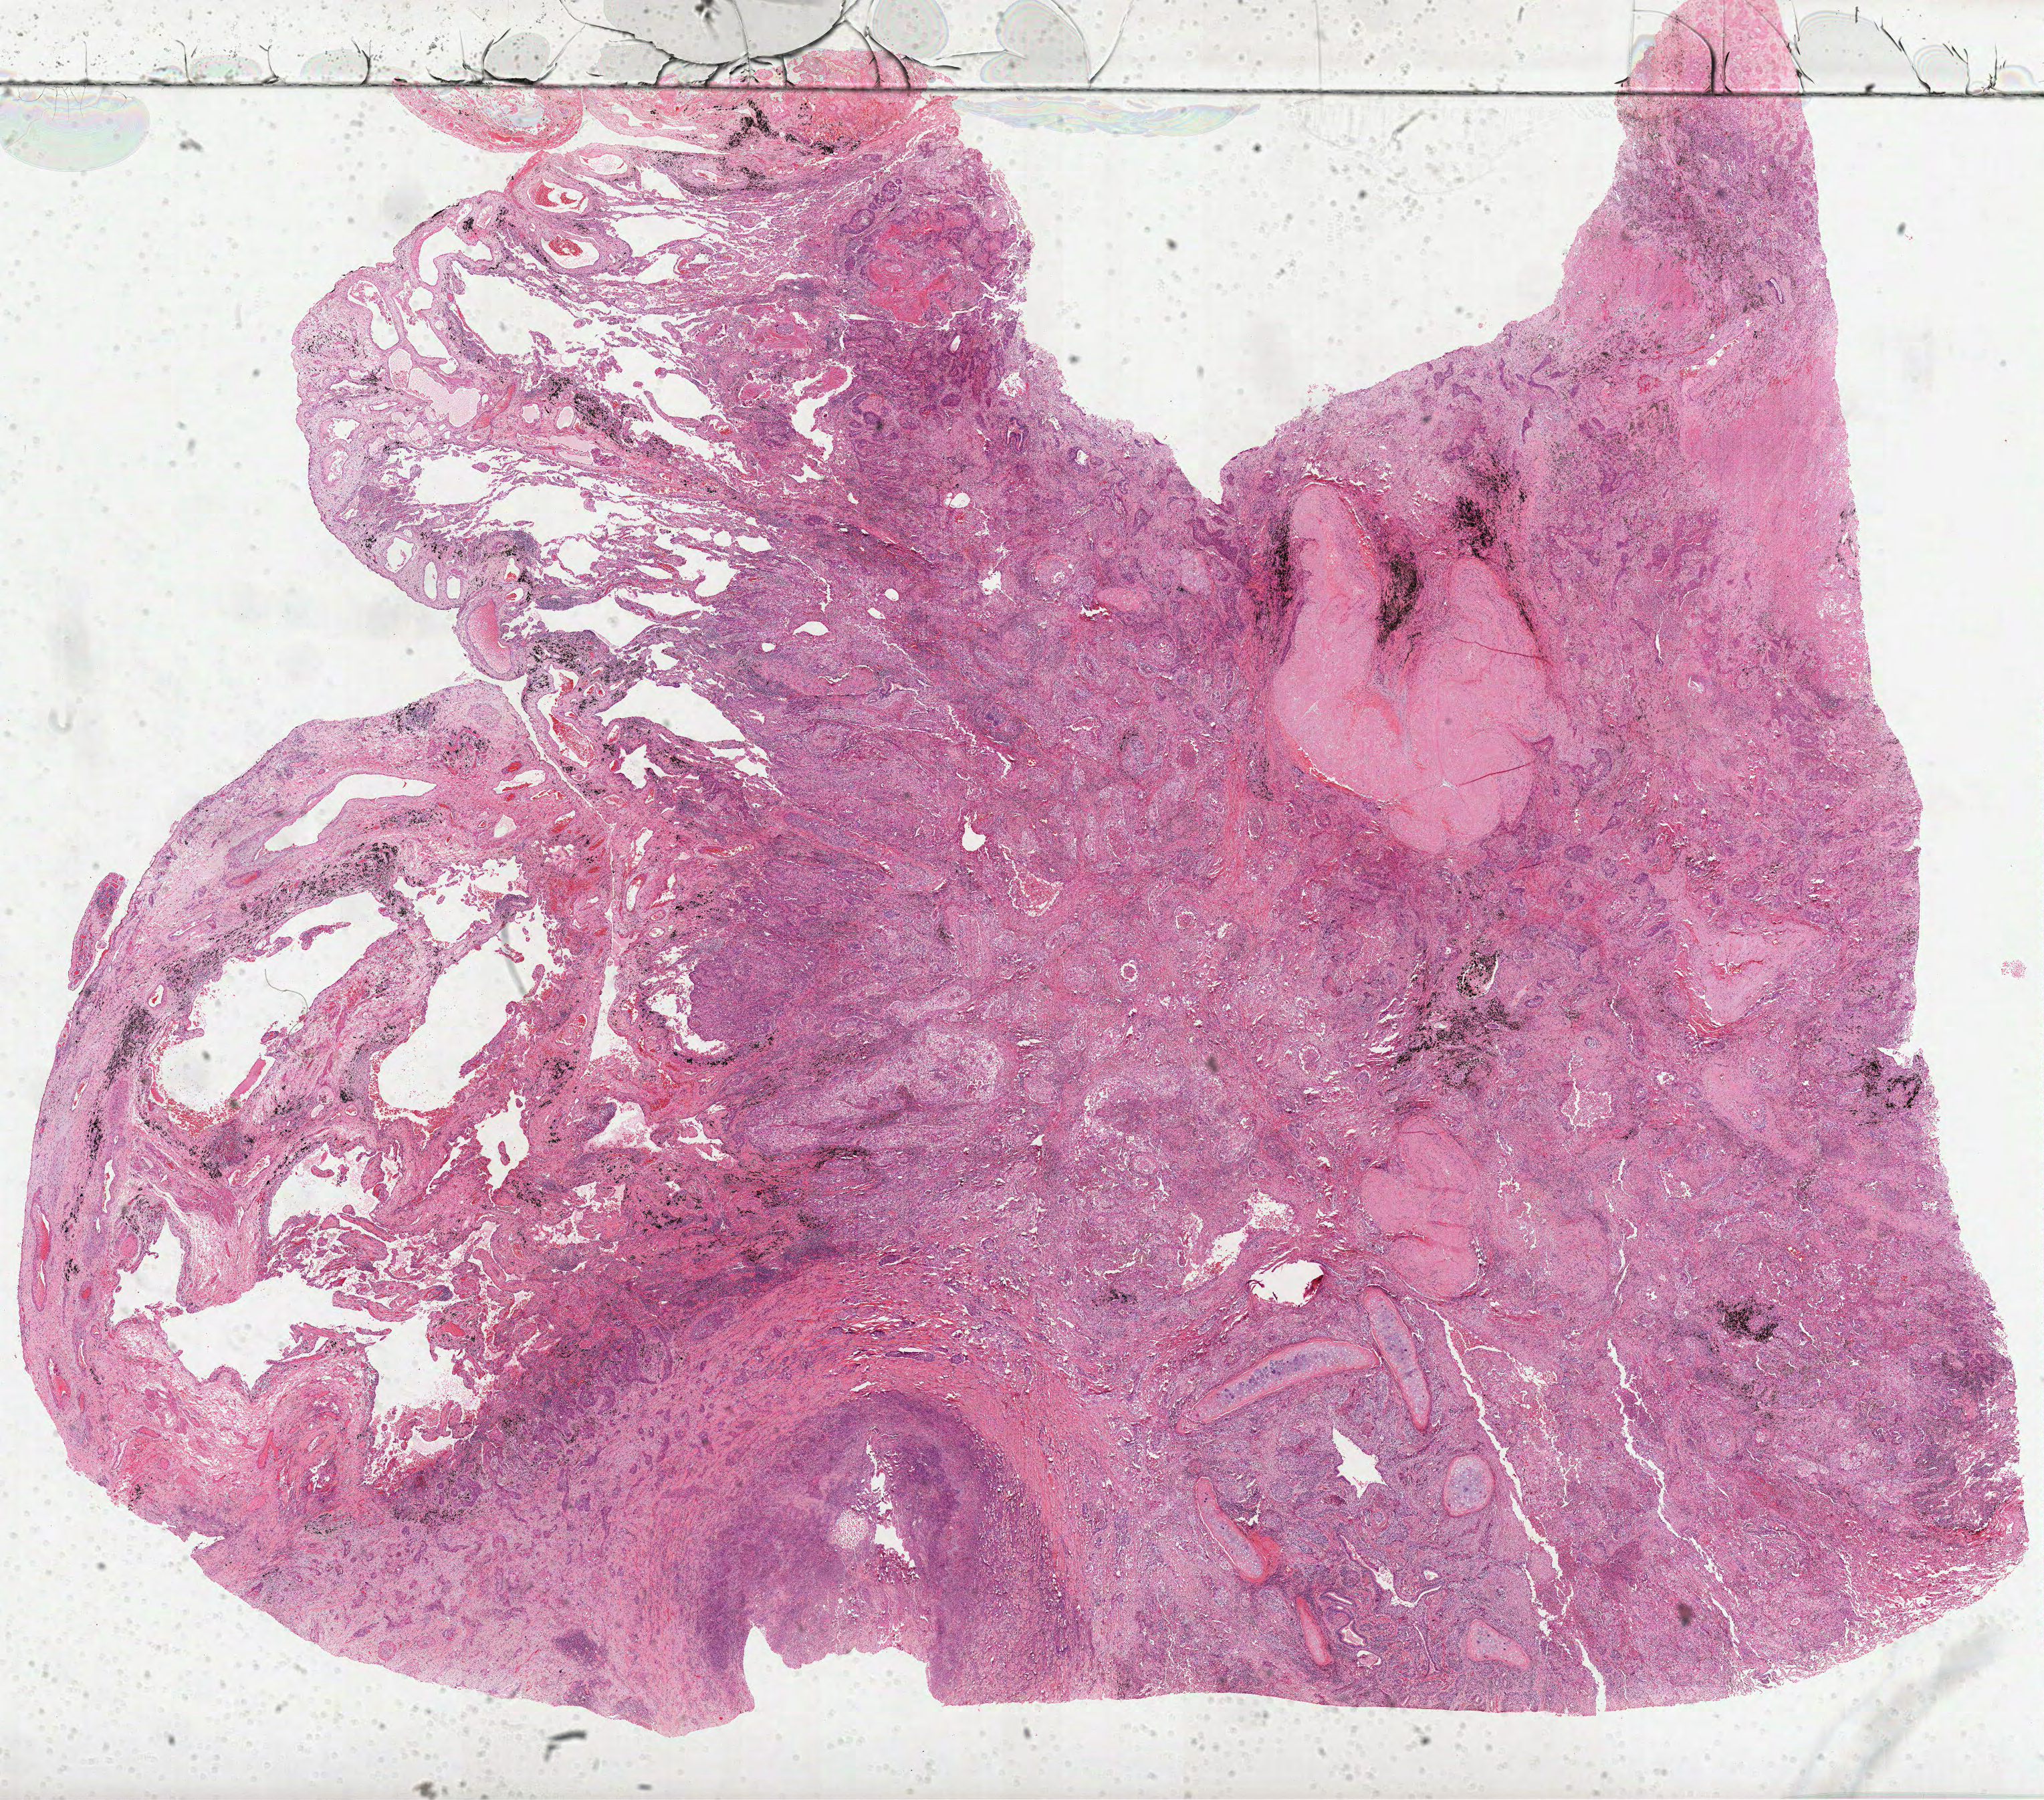
Whole-slide histology image, H&E-stained, shown as a low-resolution overview of the whole scanned area (about 24.7 x 21.7 mm); formalin-fixed paraffin-embedded (FFPE) diagnostic section; sample: primary tumour, lung. Patient: male, age at initial diagnosis 73 years.
* AJCC pathologic stage: IIIB (6th edition)
* pathologic diagnosis: Squamous cell carcinoma, NOS